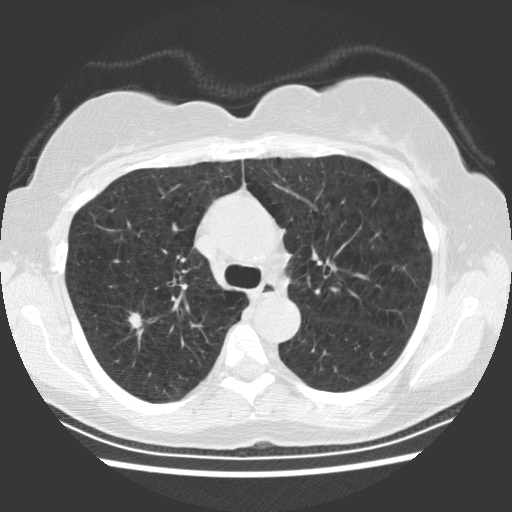
Low-dose screening chest CT, one axial slice. Slice 162 of 234 in the series (ordered by position). Reconstruction kernel STANDARD. Lung window (W 1500 / L -600 HU). 512 × 512 image matrix, field of view 330 × 330 mm.
Annotated regions visible in this slice (manually delineated by an expert):
- lesion 1 (tumor, upper lobe of right lung): bounding box <128,312,142,329> (left, top, right, bottom; pixels)